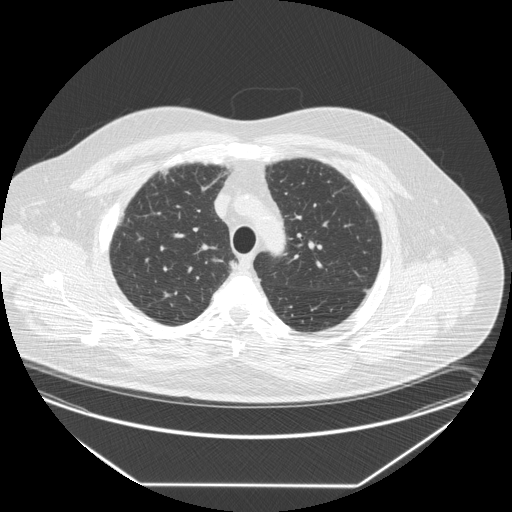
Low-dose screening chest CT, one axial slice. Slice 208 of 258 in the series (ordered by position). 120 kVp. Lung window (W 1500 / L -600 HU). 512 × 512 image matrix, field of view 440 × 440 mm.
Outlined on this slice (outlined manually by an expert reader):
- lesion 1 (tumor, upper lobe of right lung): bounding box (x1, y1, x2, y2) in pixels: (222, 261, 238, 270)